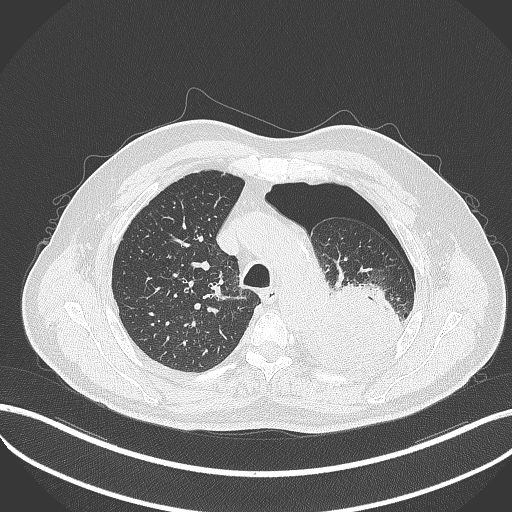
Chest CT, one axial slice; position 380 of 464 along the scan axis; lung window (W 1500 / L -600 HU); 1 mm slice thickness; 512 × 512 image matrix, field of view 400 × 400 mm. Male patient, age 76 years. From the clinical record (not read from this slice): clinical TNM (as recorded): T3 N0 M1b.
Structures marked on this image (rectangle marked by the reading radiologist):
- lung tumour (recorded histology: adenocarcinoma): bounding box <296,281,404,372> (left, top, right, bottom; pixels)